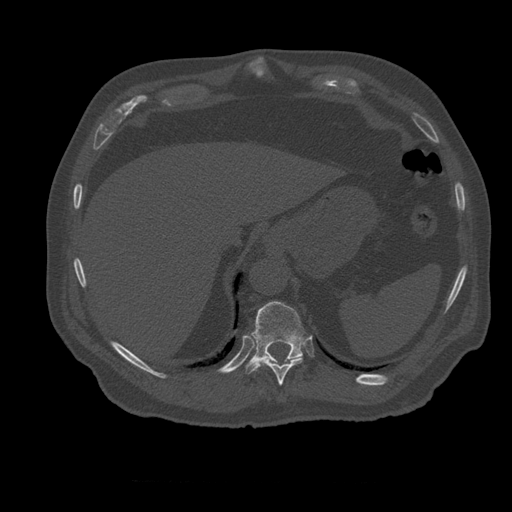
CT including the spine, one axial slice. Slice 290 of 399 in the series (ordered by position). Reconstruction kernel STANDARD. 120 kVp. Bone window (W 1800 / L 400 HU). 1.25 mm slice thickness. 512 × 512 image matrix. Patient age 73 years. Case-level facts recorded for this patient, not image findings: primary cancer: prostate.
Outlined on this slice (semi-automatic segmentation, software-assisted and operator-edited):
- T10 vertebra: box from (x=259, y=356) to (x=303, y=386) px
- T11 vertebra: (x=246, y=301)–(x=305, y=374)